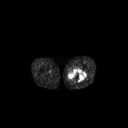
FDG PET of an extremity soft-tissue mass (from a PET/CT study), one axial slice; position 243 of 267 along the scan axis; 3.27 mm slice thickness; 128 × 128 image matrix, field of view 700 × 700 mm. Male patient, age 44 years. Case-level facts recorded for this patient, not image findings: histological type: undifferentiated pleomorphic liposarcoma; grade: high; site of the primary tumour: left thigh.
Structures marked on this image (expert contour drawn on MRI and transferred to this co-registered scan by the dataset authors):
- gross tumour volume including surrounding oedema: bounding box [x1, y1, x2, y2] px = [67, 69, 86, 83]
- gross tumour volume (mass): [68, 69, 86, 82]